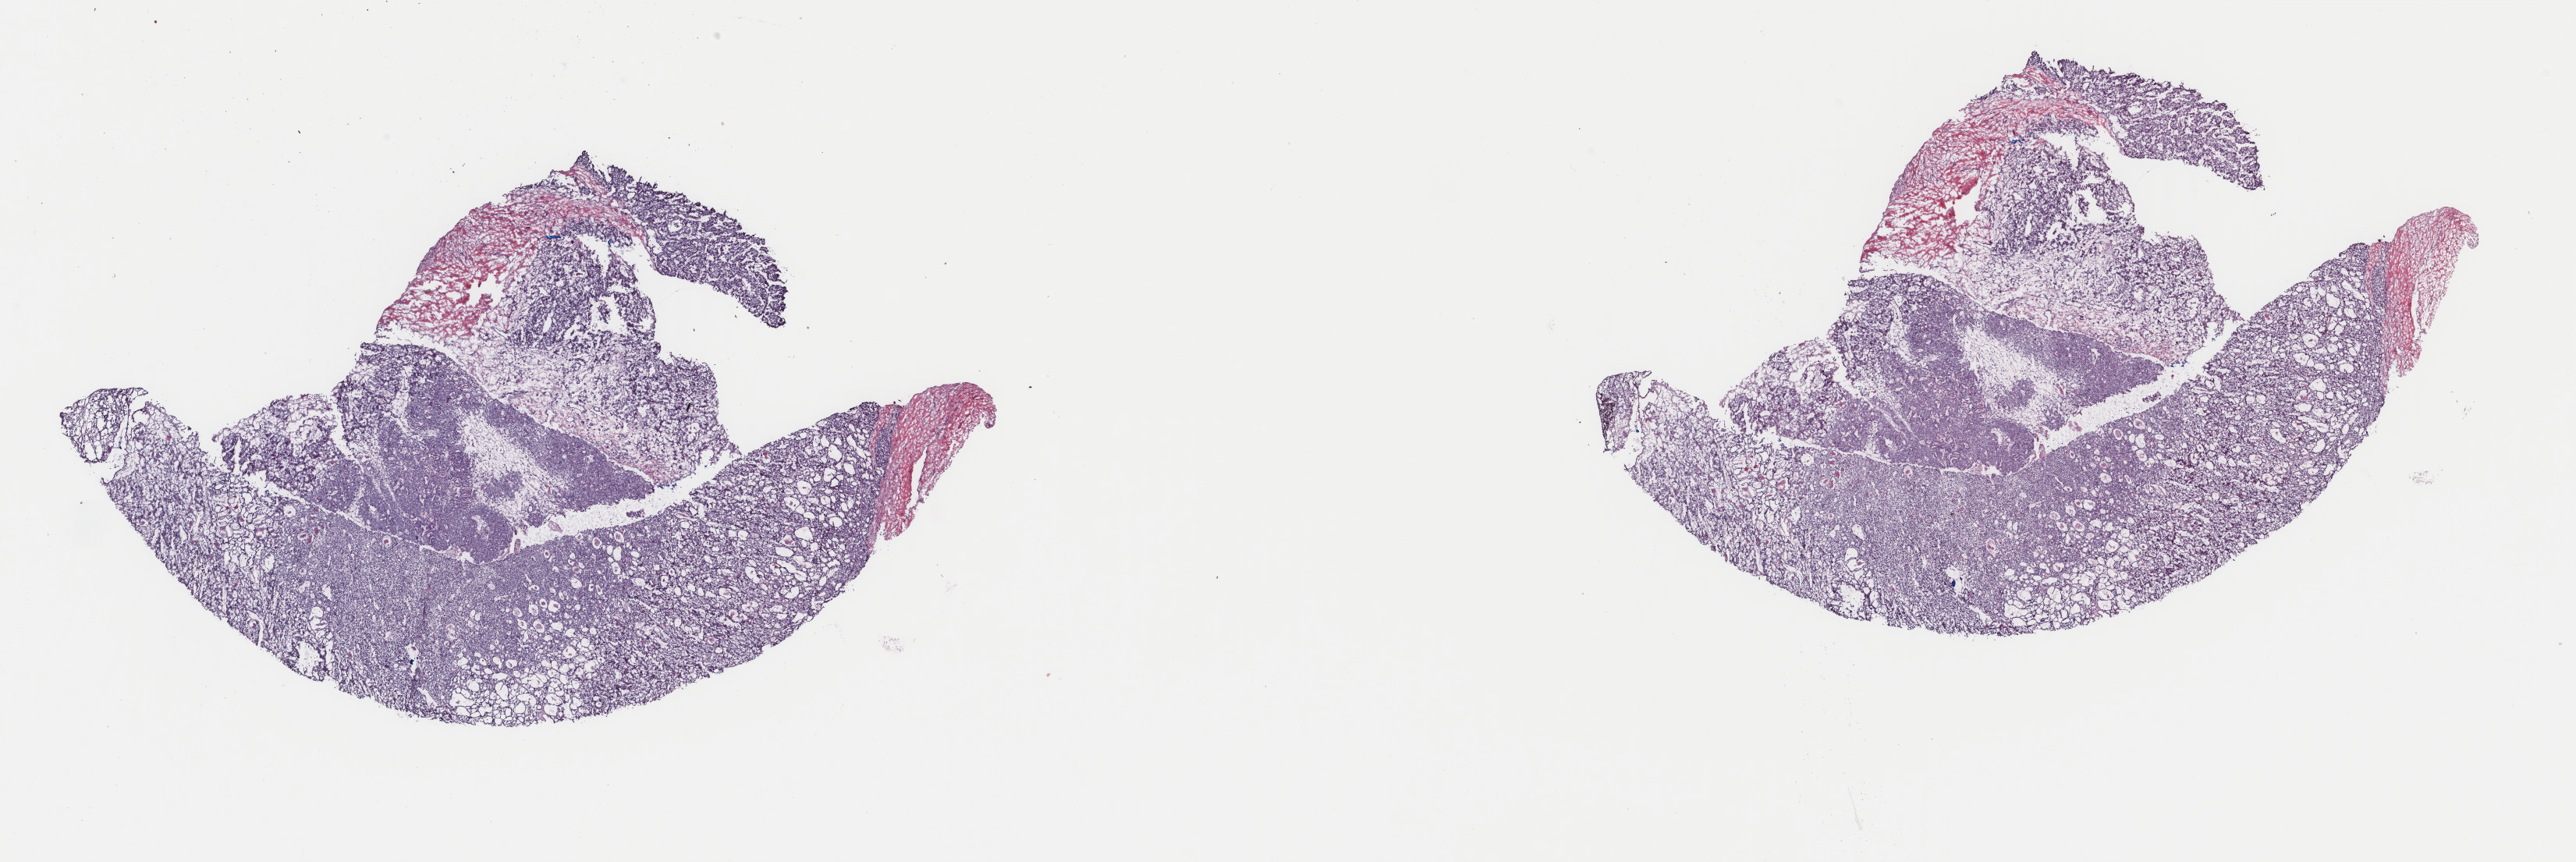
H&E whole-slide image, a low-resolution overview of the entire scanned area, about 26.2 x 8.8 mm, frozen section, thyroid, primary tumour sample. Male patient; age at initial diagnosis 28 years. Pathologist review of this section (percent, as recorded): tumour cells 80%, tumour nuclei 100%, normal cells 0%, stromal cells 20%, necrosis 0%. Infiltration values recorded for this section: lymphocyte infiltration 1%, monocyte infiltration 0%, neutrophil infiltration 0%.
• histologic diagnosis: Papillary adenocarcinoma, NOS (thyroid gland)
• AJCC pathologic stage: I (7th edition)